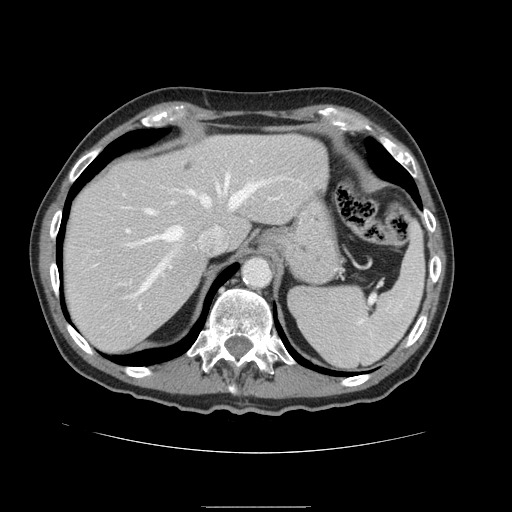
Contrast-enhanced abdominal CT, one axial slice. Slice 119 of 168 in the series (ordered by position). 120 kVp. Intravenous contrast given. Soft-tissue window (W 400 / L 40 HU). 512 × 512 image matrix, field of view 386 × 386 mm. Male patient, age 74 years. Case-level facts recorded for this patient, not image findings: diagnosis: colorectal cancer liver metastases, imaged before liver resection; multiple liver metastases: no; largest metastasis: 14.5 cm; disease in both lobes: yes.
Structures marked on this image (manually delineated by an expert):
- hepatic veins: bounding box [x1, y1, x2, y2] px = [128, 176, 291, 298]
- liver: [63, 135, 328, 354]
- planned liver remnant (the part of the liver to remain after resection): [63, 134, 327, 353]
- portal vein (with intrahepatic branches): [128, 198, 277, 232]